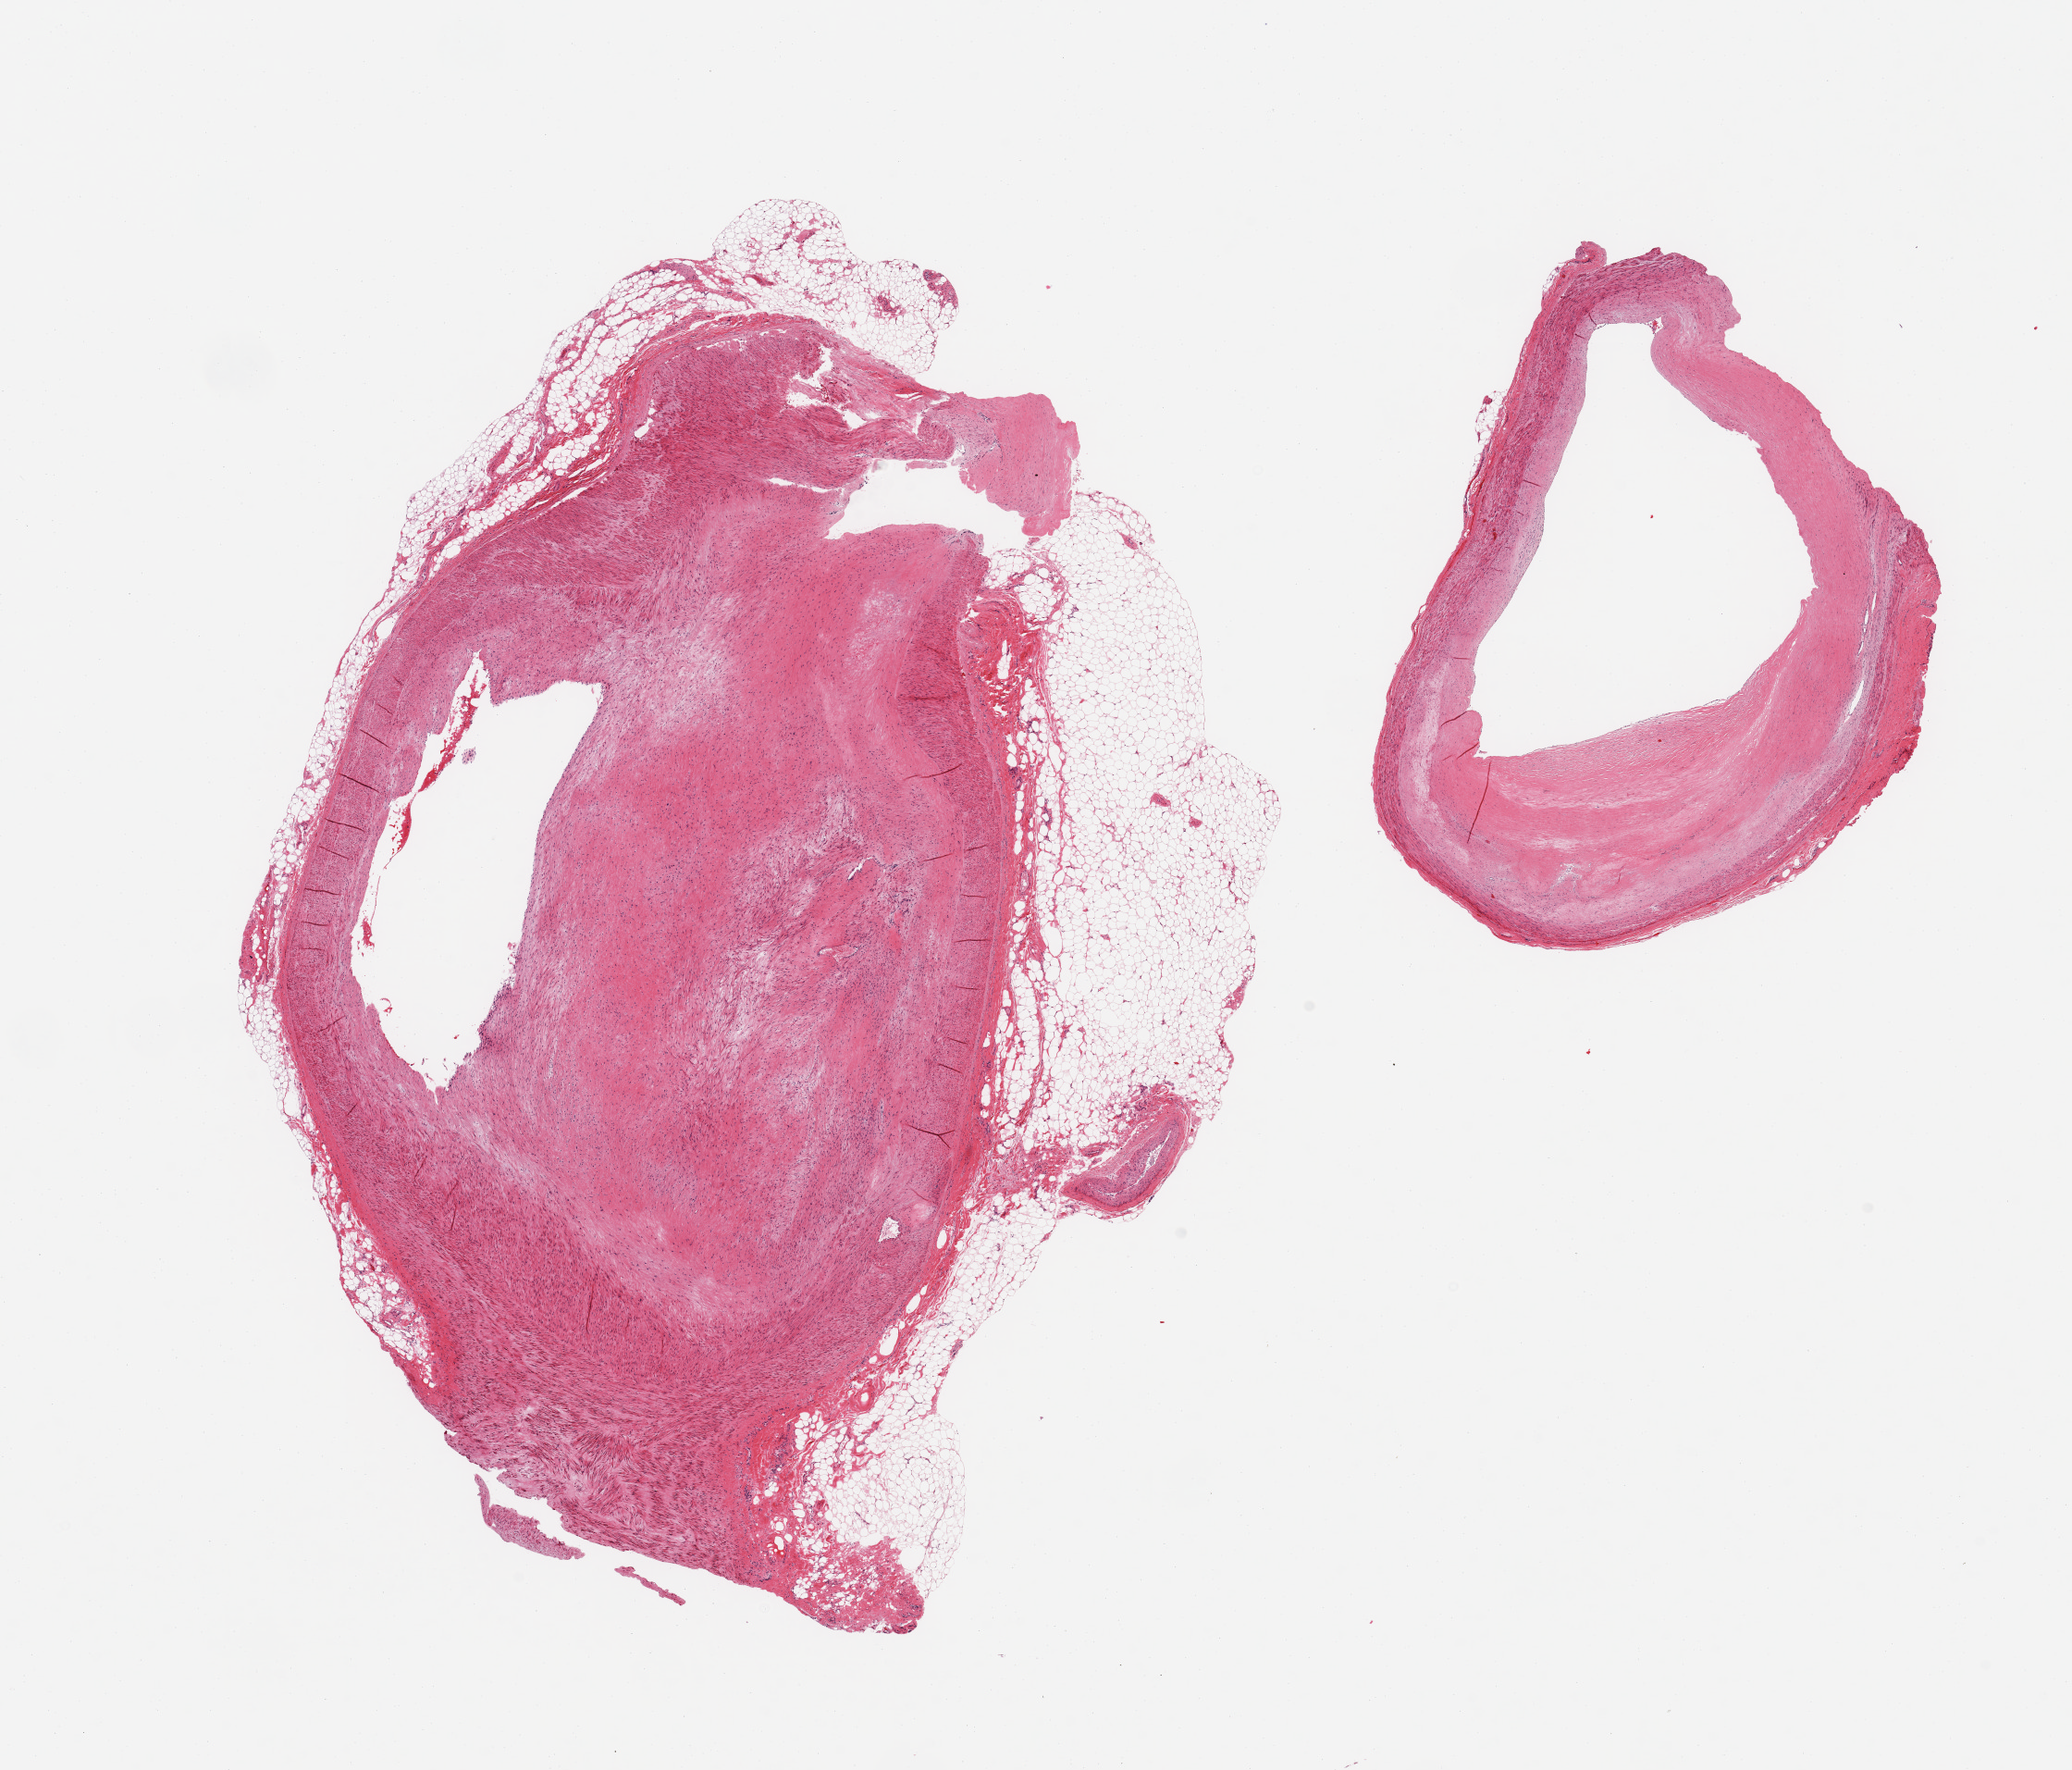
Digitized H&E-stained section — low-resolution overview of the scanned area, about 17.7 x 15.1 mm (acquisition: 20x scan); PAXgene-fixed, paraffin-embedded tissue; sampled site (target tissue): coronary artery; donor tissue sample. Male donor.
Review note (as recorded): 2 pieces, ~80% luminal occlusive atherosis; adhereant fat up to ~1.5mm.